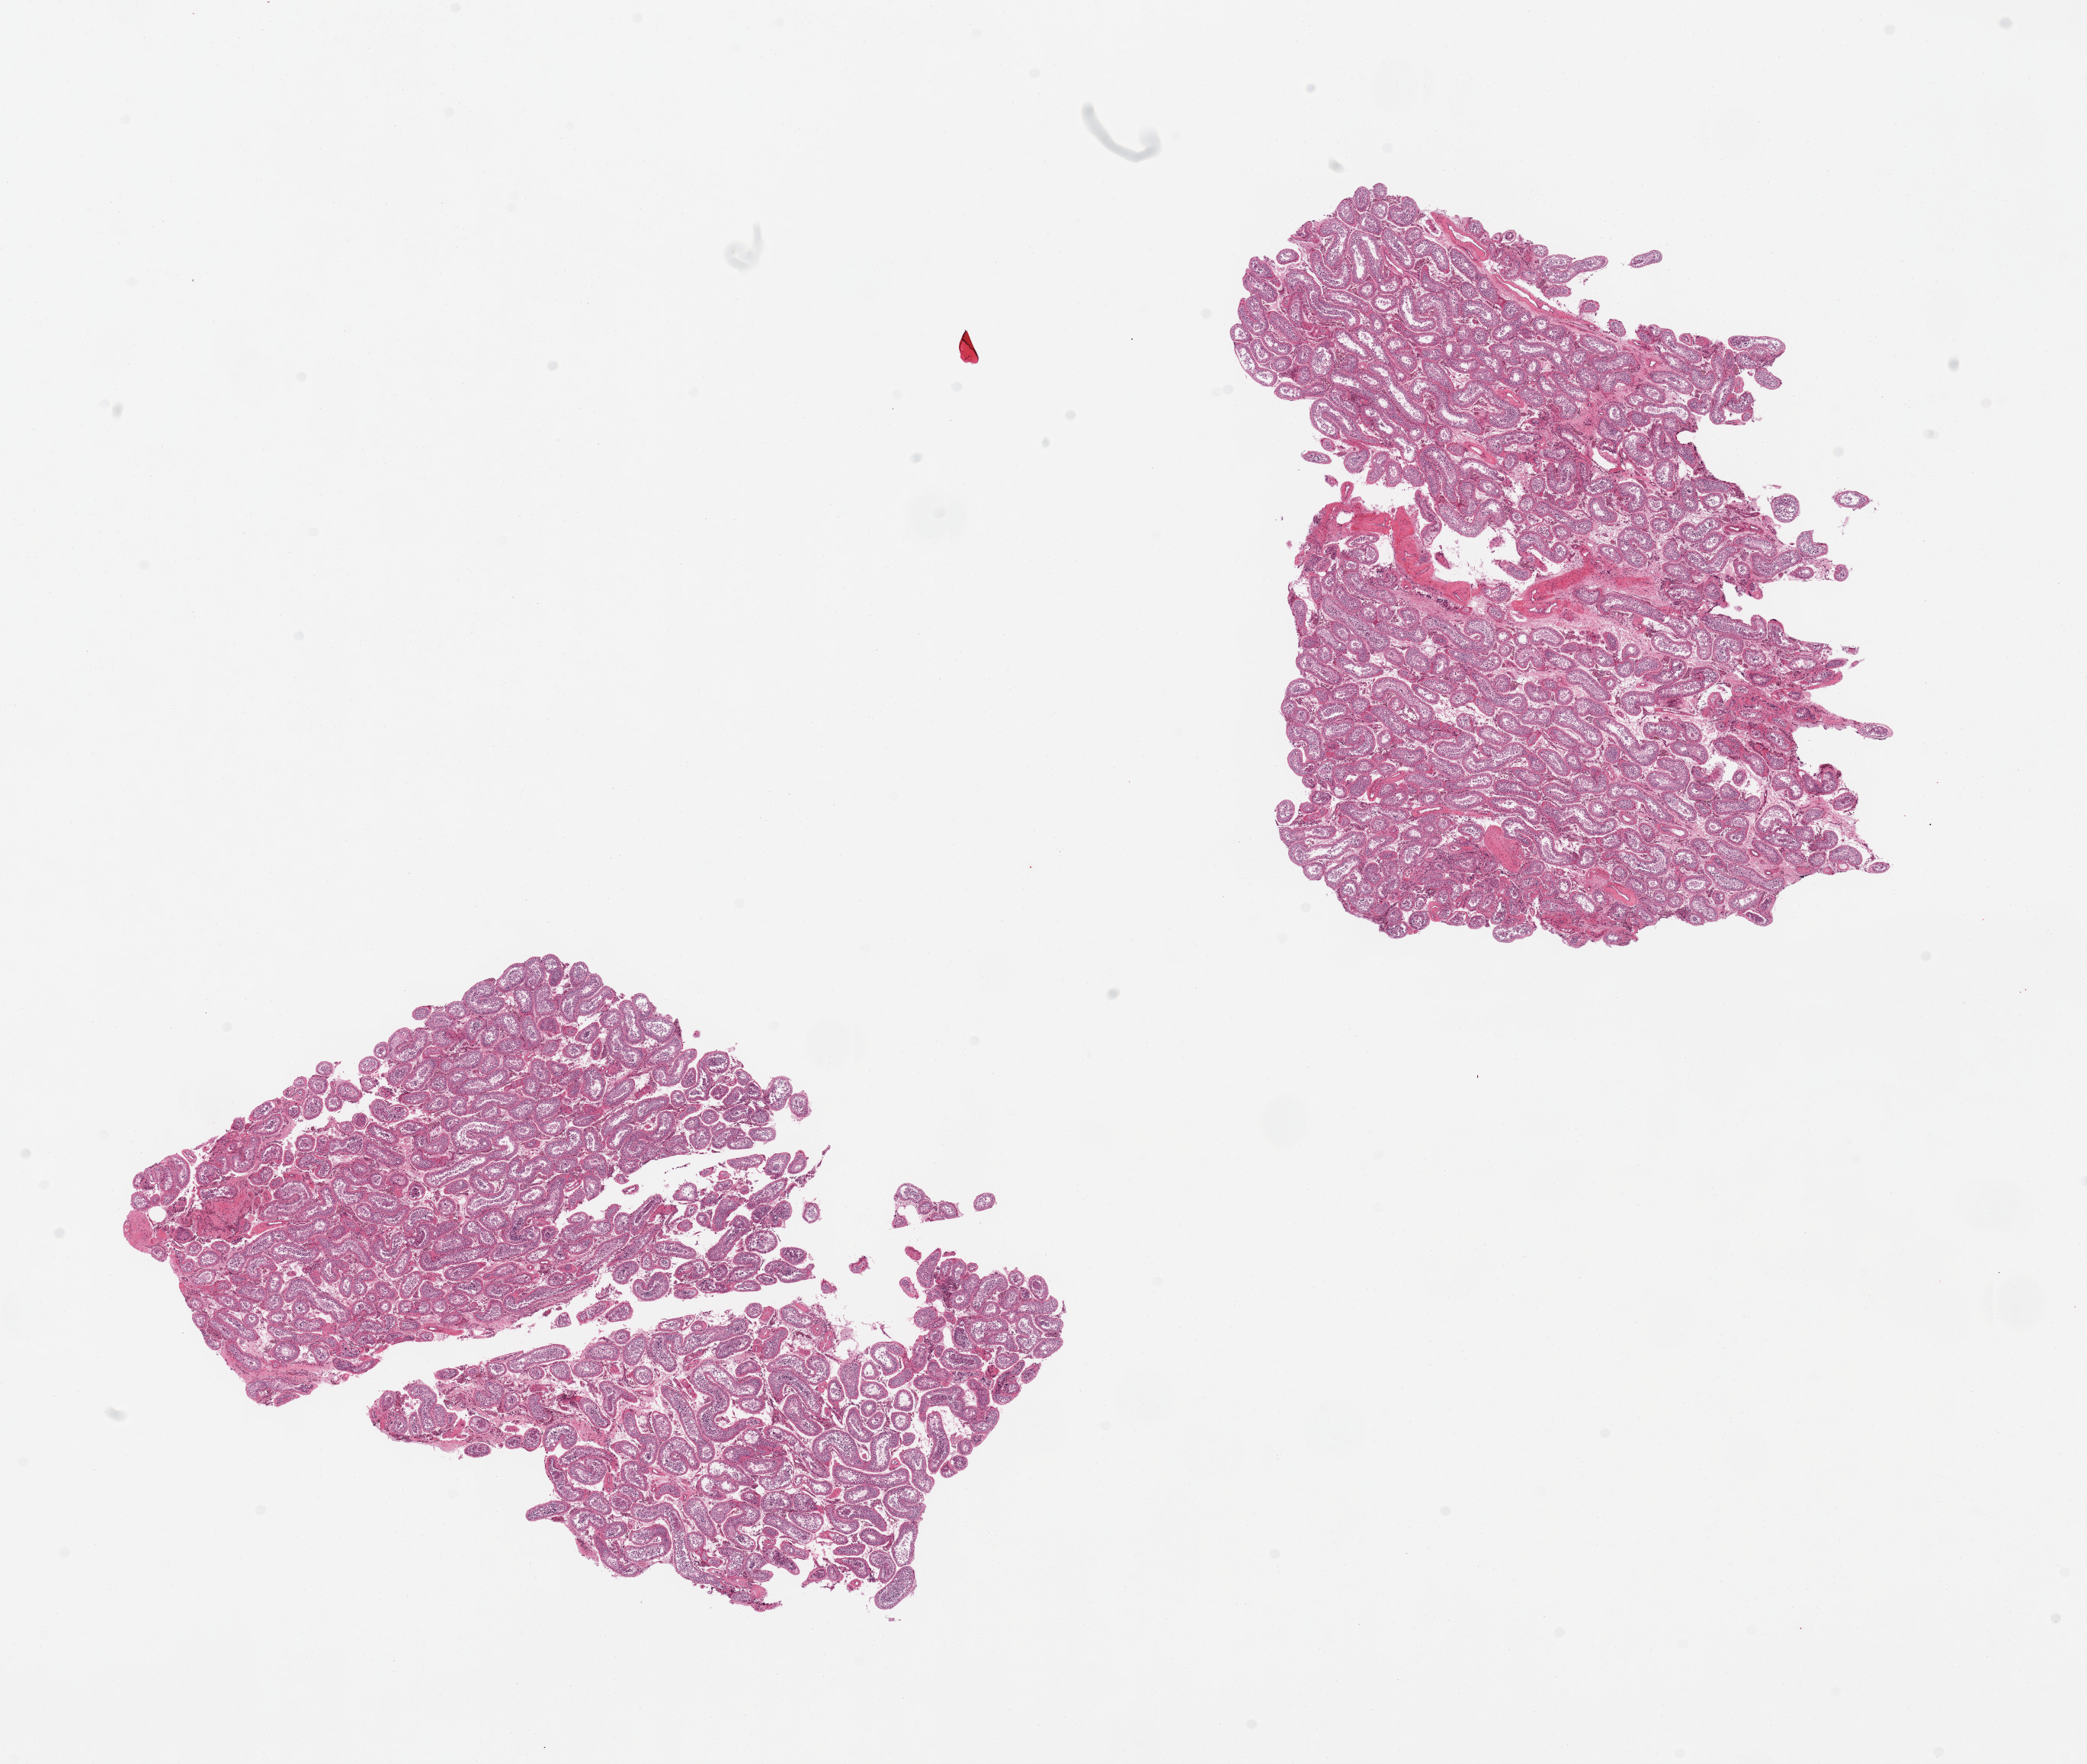
Digitized H&E-stained section, low-resolution overview of the scanned area, about 21.7 x 18.3 mm (acquisition: 20x scan). PAXgene-fixed, paraffin-embedded tissue. Target tissue: testis. Donor tissue sample. Male donor.
- review note (as recorded): 2 pieces; spermatogenesis